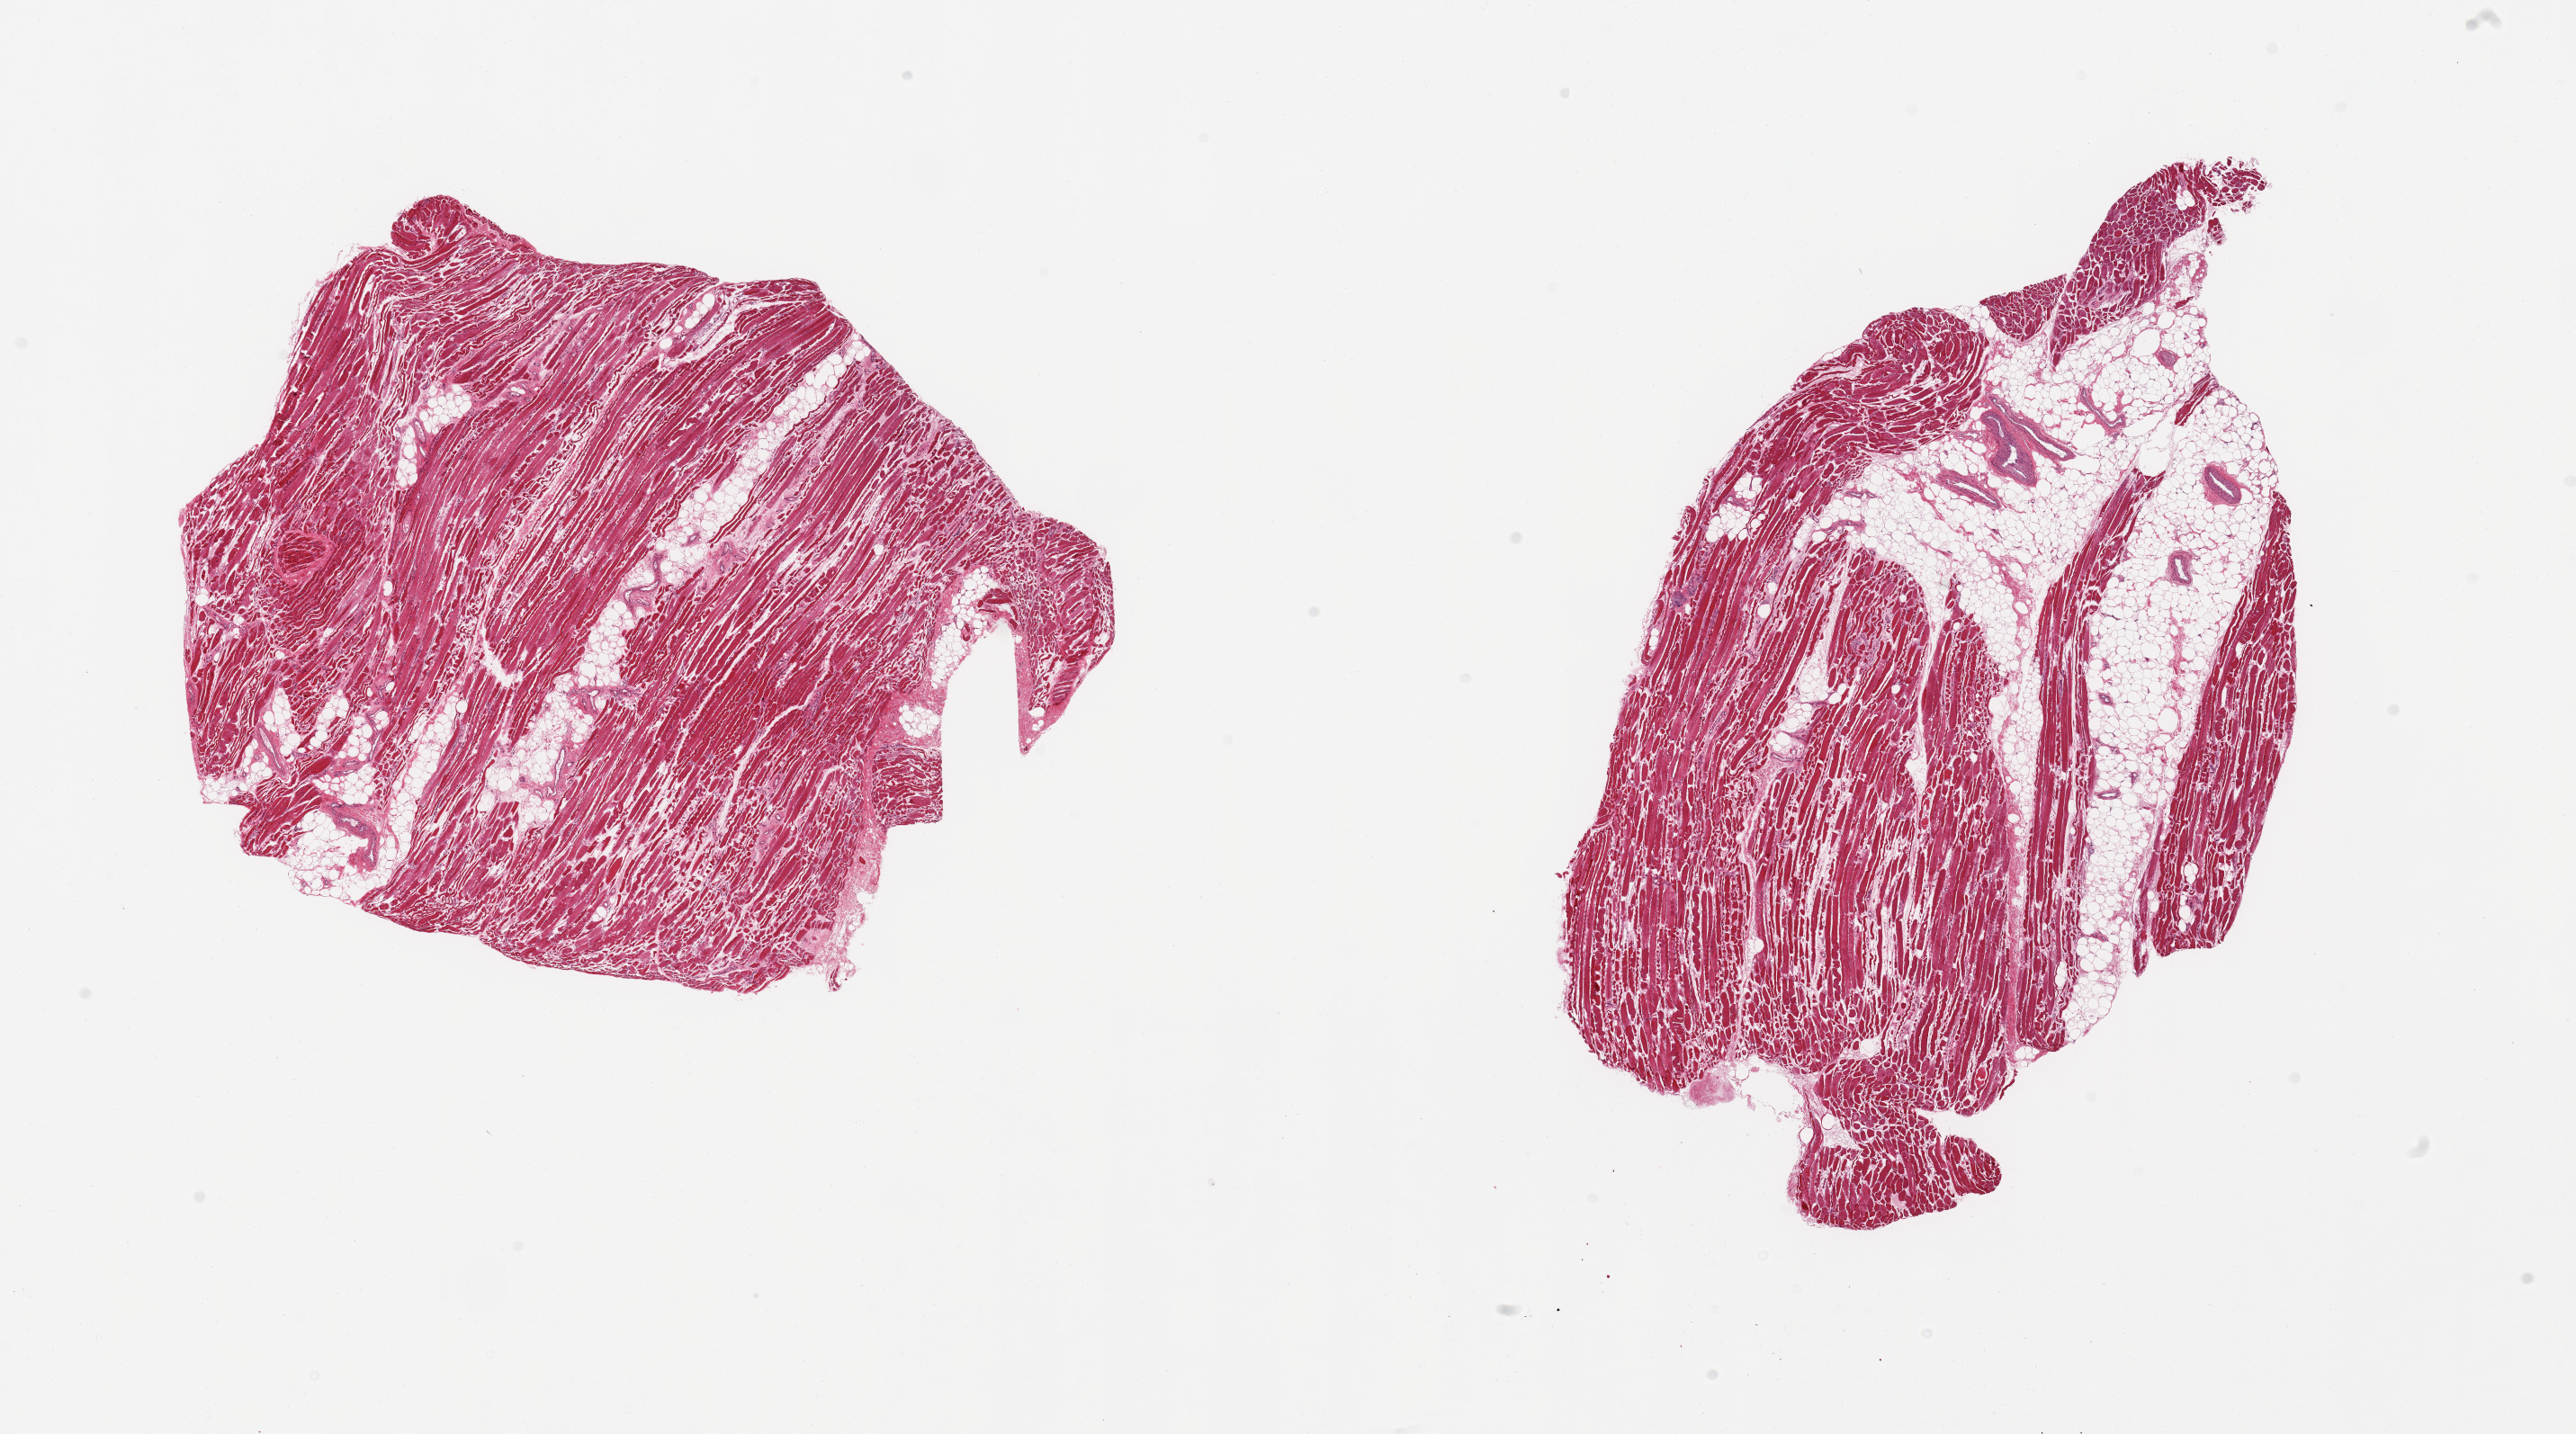
Hematoxylin and eosin (H&E) whole-slide image — low-resolution overview of the scanned area, about 22.6 x 12.6 mm (slide scanned at 20x); PAXgene-fixed, paraffin-embedded tissue; section of skeletal muscle (target tissue); tissue donor sample. Donor sex: male.
Pathologist's review note for this sample: 2 pieces, ~30% adherent/interstitial fat.